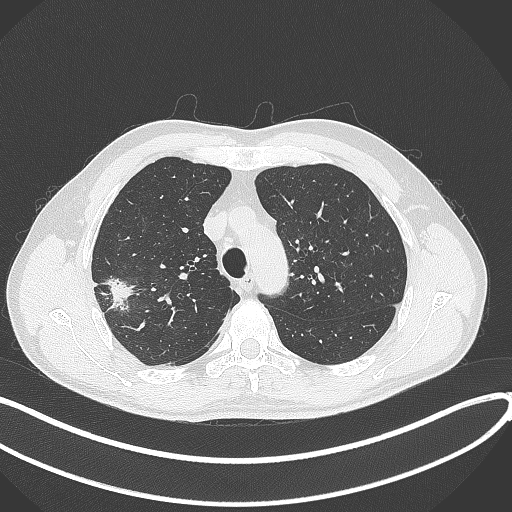
Chest CT, one axial slice; position 314 of 381 along the scan axis; reconstruction kernel B70f; 120 kVp; lung window (W 1500 / L -600 HU); 512 × 512 image matrix, field of view 400 × 400 mm. Patient: male, 62 years. From the clinical record (not read from this slice): clinical TNM (as recorded): T1c N0 M0.
Structures marked on this image (bounding box drawn by a radiologist):
- lung tumour (recorded histology: adenocarcinoma): box from (x=101, y=271) to (x=136, y=313) px